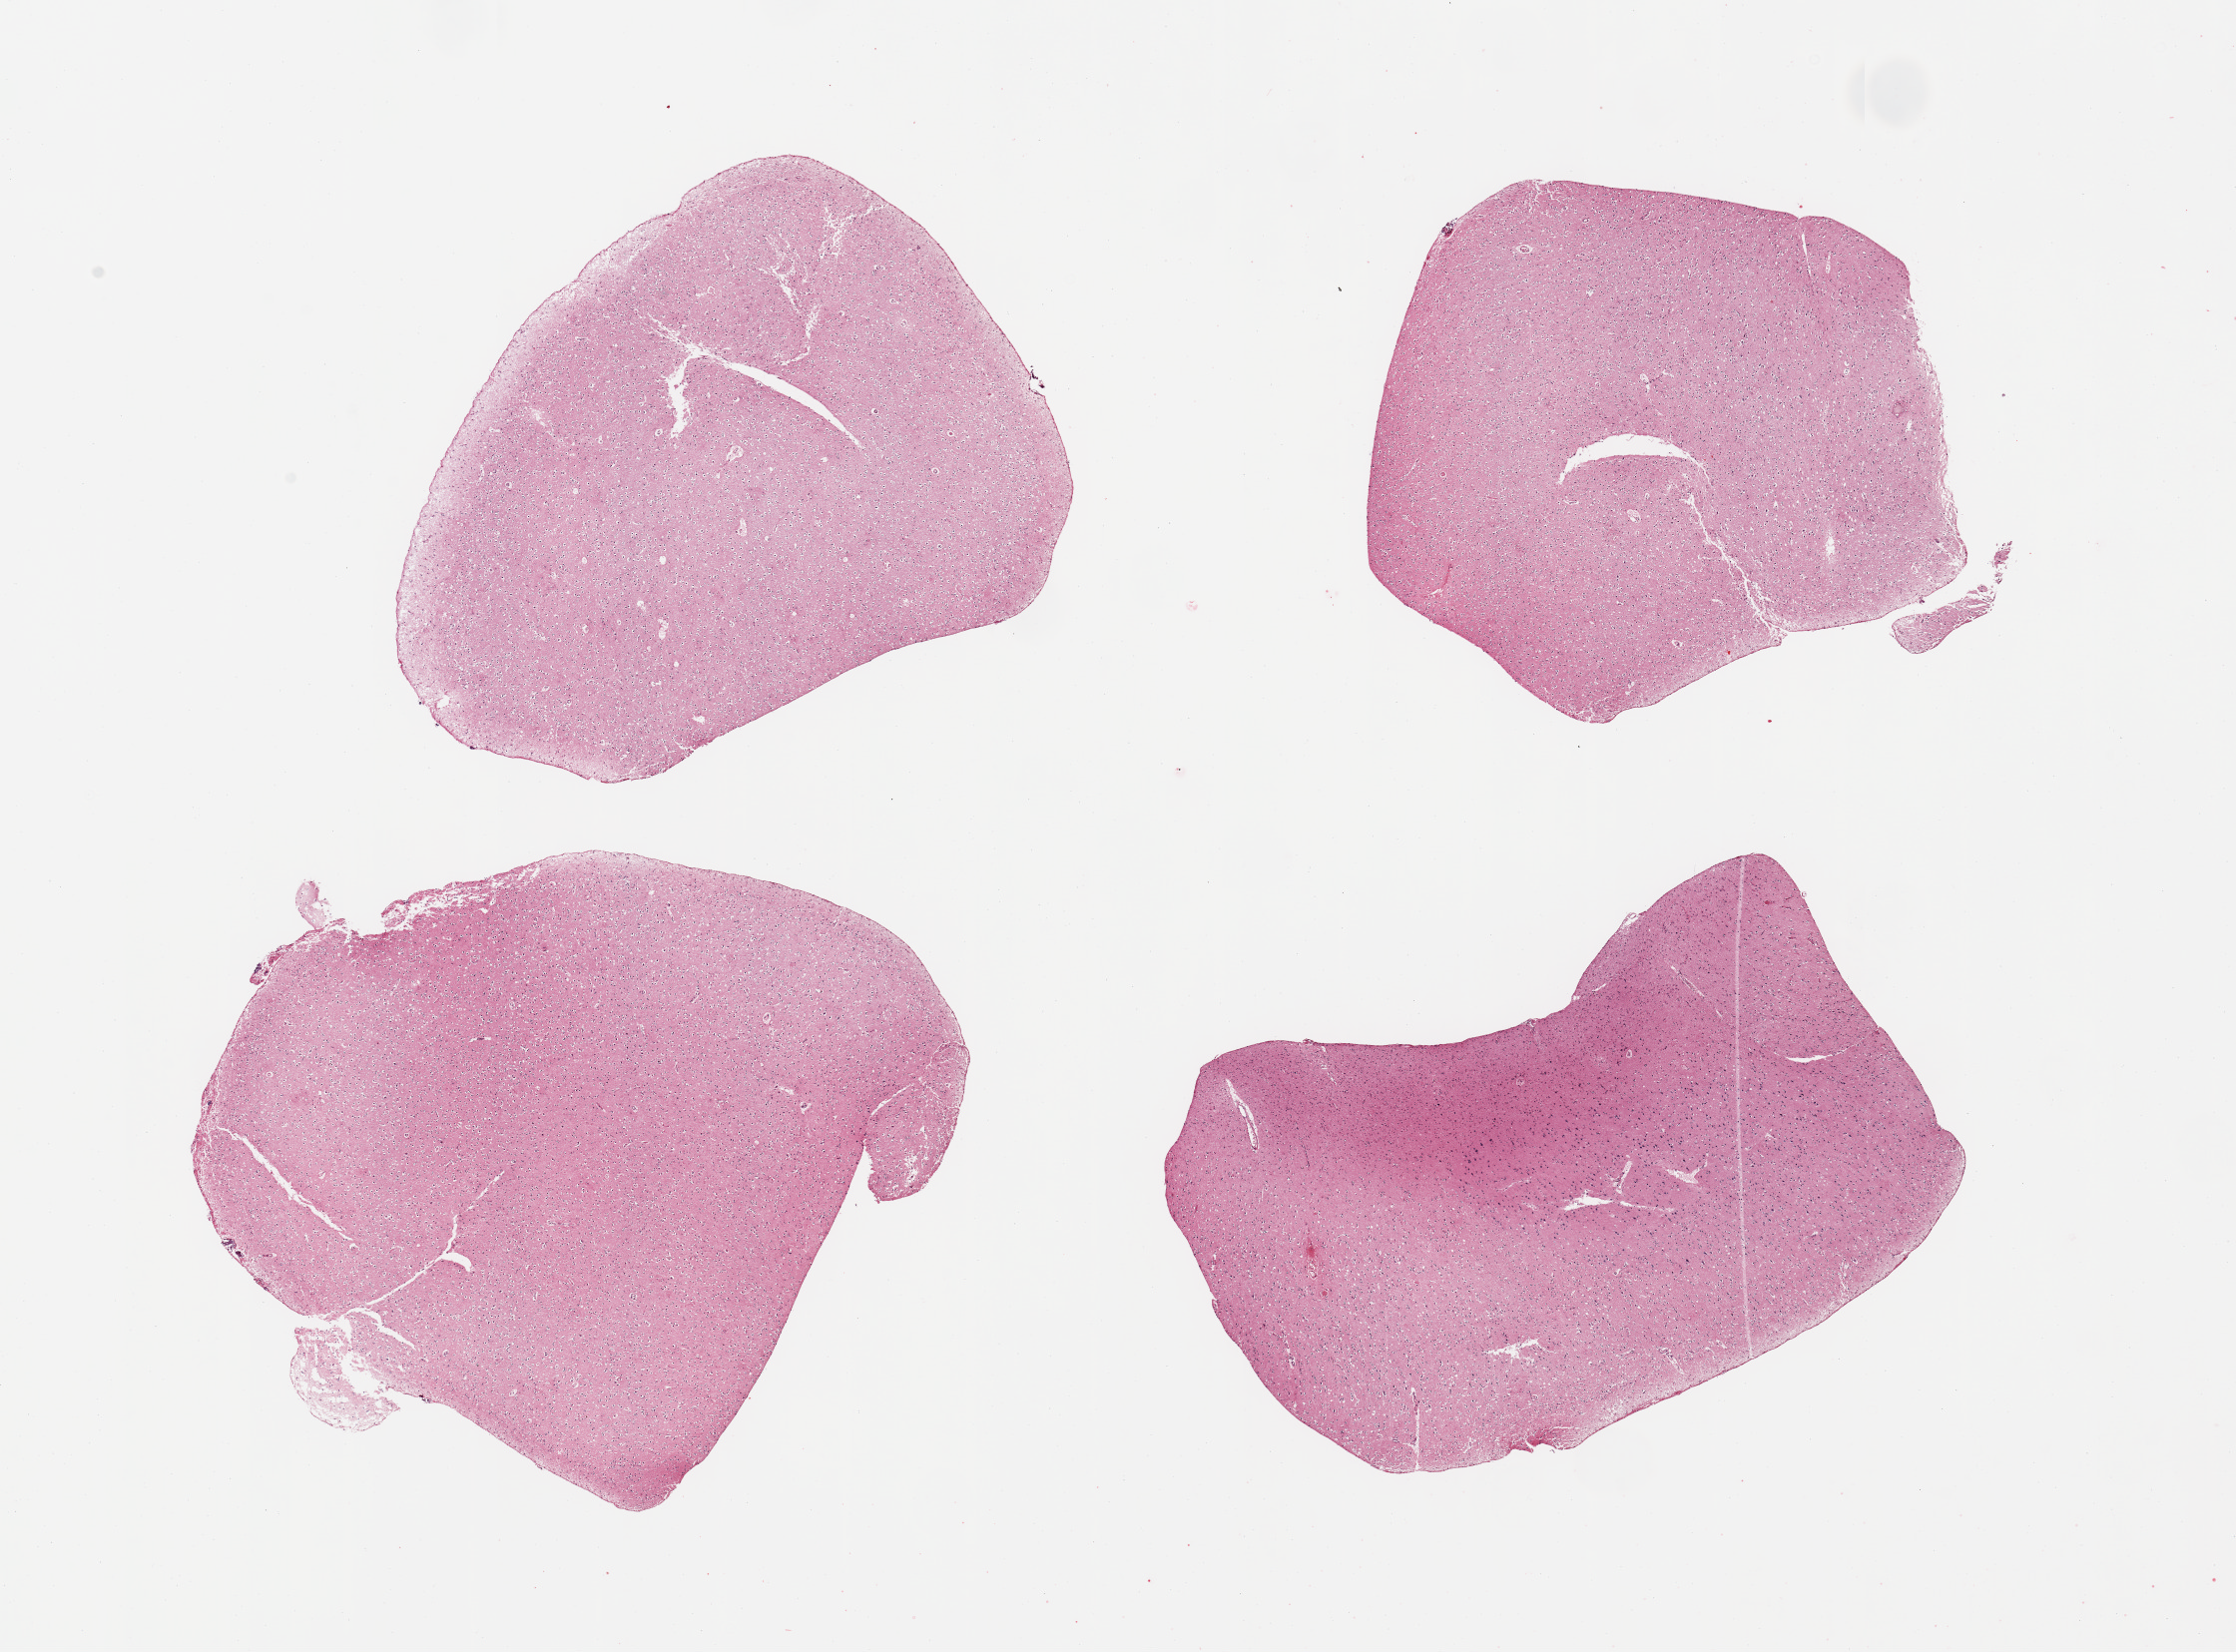
Digitized H&E-stained section — low-resolution overview of the scanned area, about 17.7 x 13.1 mm (acquisition: 20x scan). PAXgene-fixed paraffin-embedded (PFPE) section. Sampled site (target tissue): cerebral cortex. Tissue donor sample. Female donor.
• pathologist's review note for this sample: 4 pieces